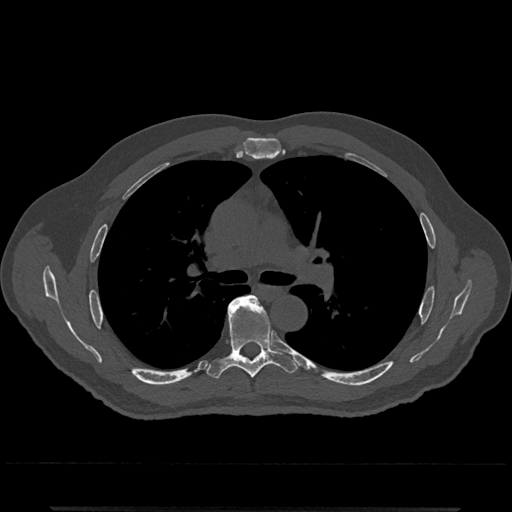
CT including the spine, one axial slice. Reconstruction kernel Br40s/3. 120 kVp. Bone window (W 1800 / L 400 HU). 0.5 mm slice thickness. 512 × 512 image matrix, field of view 393 × 393 mm. Male patient, age 67 years. From the clinical record (not read from this slice): primary cancer: prostate.
Outlined on this slice (semi-automatically segmented with operator editing):
- T5 vertebra: bounding box [x1, y1, x2, y2] px = [245, 296, 258, 302]
- T6 vertebra: [206, 295, 298, 379]